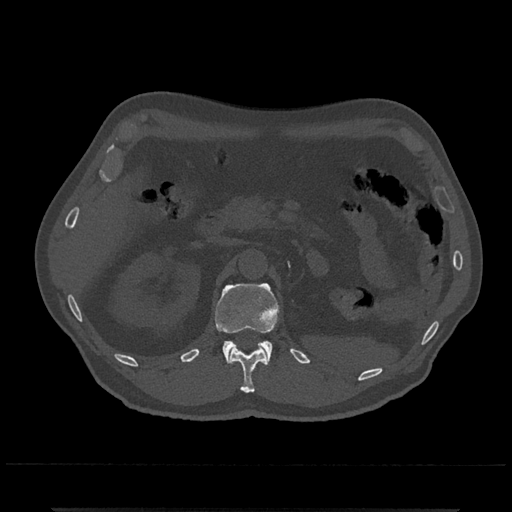
CT including the spine, one axial slice; slice 394 of 797 in the series (ordered by position); reconstruction kernel Br40s/3; bone window (W 1800 / L 400 HU); 0.5 mm slice thickness; 512 × 512 image matrix, field of view 393 × 393 mm. Male patient, age 67 years. From the clinical record (not read from this slice): primary cancer: prostate.
Structures marked on this image (semi-automatic segmentation, software-assisted and operator-edited):
- L1 vertebra: bounding box [x1, y1, x2, y2] px = [214, 283, 280, 363]
- T12 vertebra: [229, 346, 268, 393]